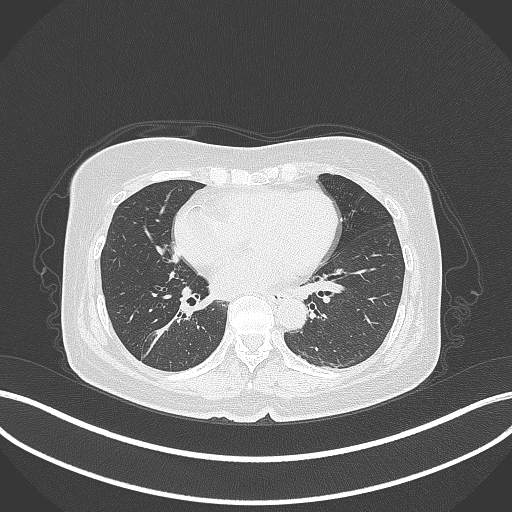
Chest CT, one axial slice; position 172 of 429 along the scan axis; reconstruction kernel B70f; 120 kVp; lung window (W 1500 / L -600 HU); 512 × 512 image matrix, field of view 400 × 400 mm. Female patient, age 67 years. From the clinical record (not read from this slice): clinical TNM (as recorded): T1c N1 M0.
Annotated regions visible in this slice (bounding box drawn by a radiologist):
- lung tumour (recorded histology: adenocarcinoma): bounding box <146,306,187,350> (left, top, right, bottom; pixels)